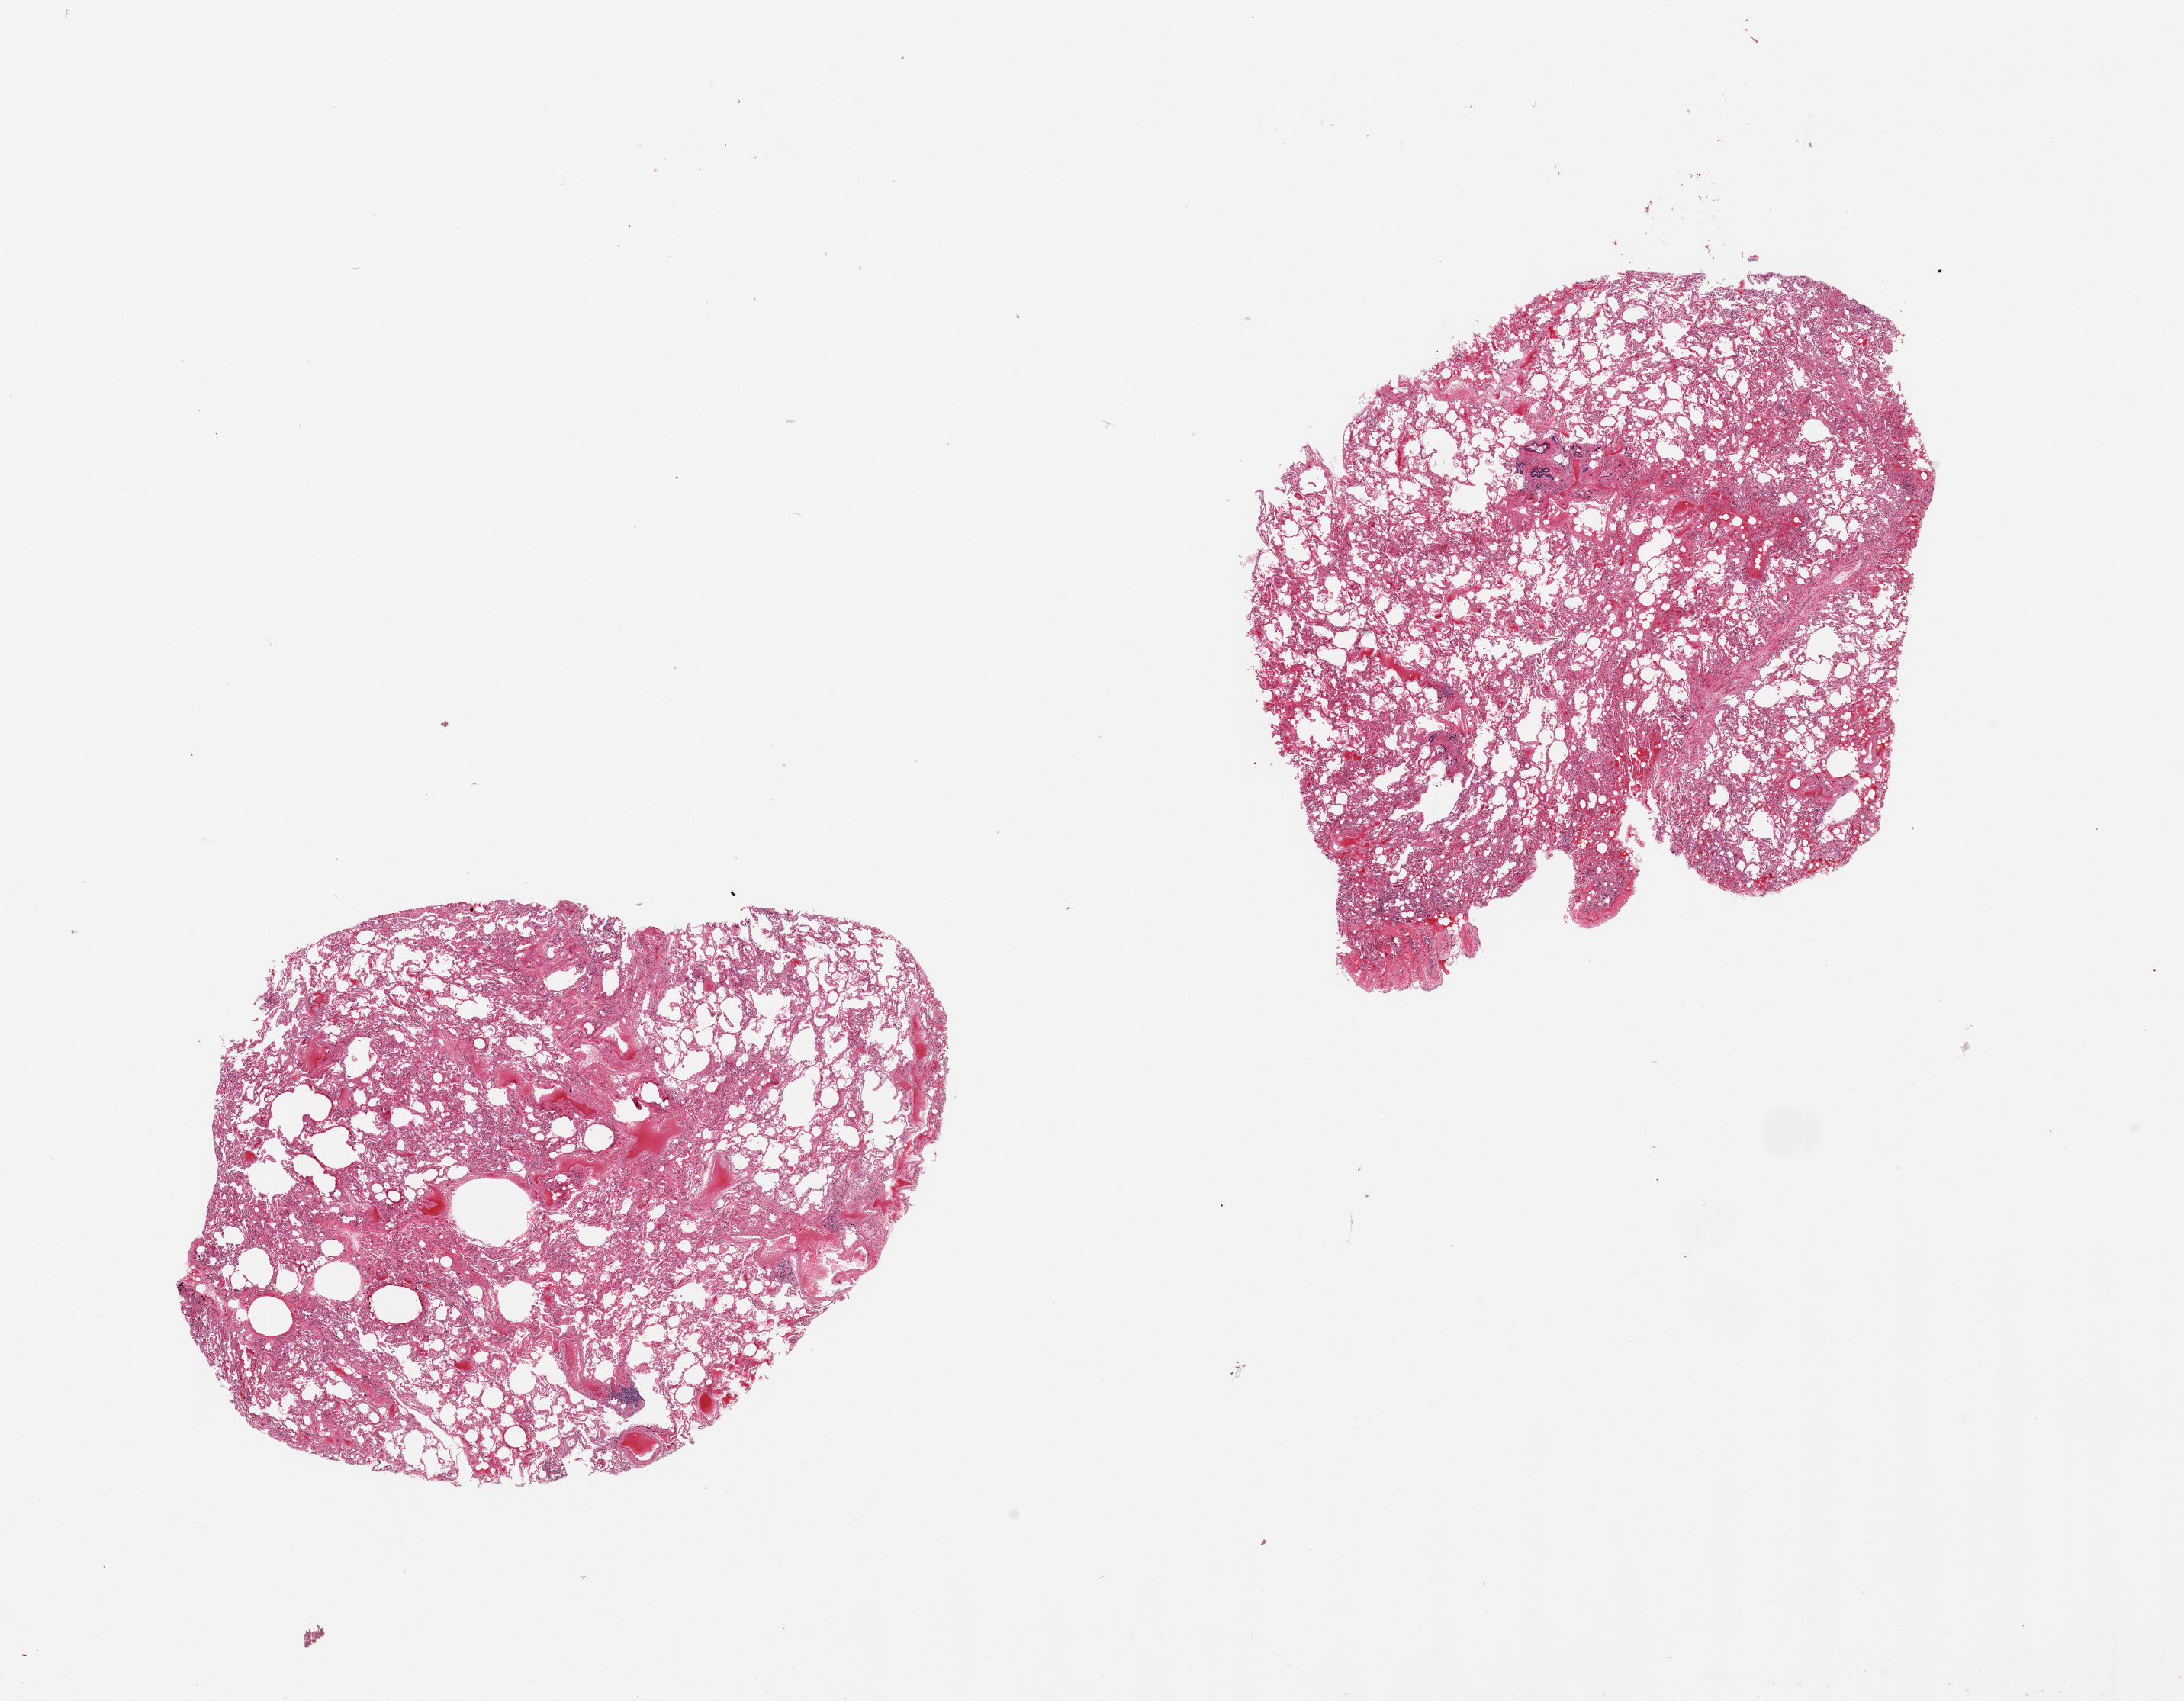
Digitized haematoxylin and eosin-stained section — whole scanned area (about 22.6 x 17.6 mm) shown as a low-resolution overview. PAXgene-fixed paraffin-embedded (PFPE) section. Sampled site (target tissue): lung. Tissue donor sample. Donor sex: female.
• reviewer comment on this tissue sample: 2 pieces, patchy congestion/edema